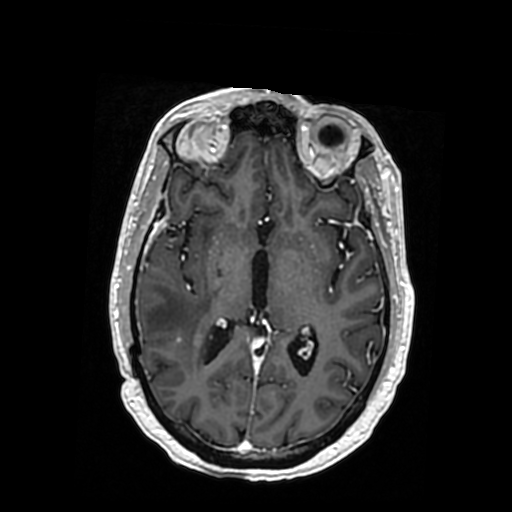
Brain MRI from a brain-tumour surgery series, one axial slice. Position 187 of 364 along the scan axis. T1-weighted post-contrast. 0.5 mm slice thickness. 512 × 512 image matrix. Case-level facts recorded for this patient, not image findings: histopathology: Oligodendroglioma; WHO grade: 3; IDH mutation: yes.
Structures marked on this image (expert manual segmentation):
- tumour: bounding box (x1, y1, x2, y2) in pixels: (188, 335, 212, 342)